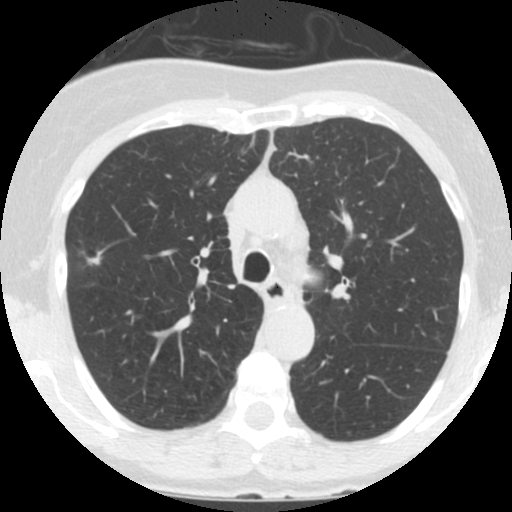
Low-dose screening chest CT, one axial slice; position 100 of 146 along the scan axis; reconstruction kernel STANDARD; 120 kVp; lung window (W 1500 / L -600 HU); 512 × 512 image matrix, field of view 280 × 280 mm.
Structures marked on this image (outlined manually by an expert reader):
- lesion 1 (tumor, upper lobe of right lung): bounding box [x1, y1, x2, y2] px = [87, 253, 101, 265]